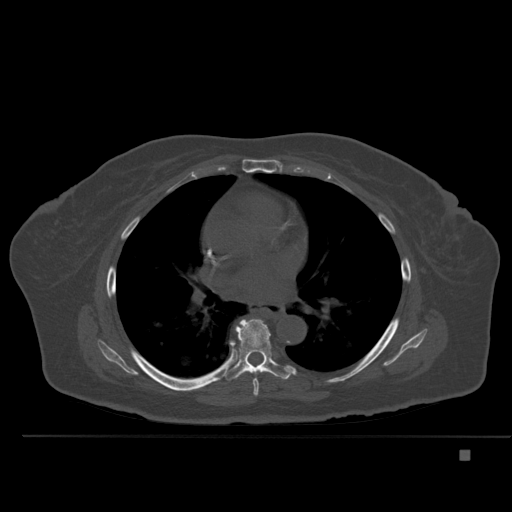
CT including the spine, one axial slice; slice 329 of 477 in the series (ordered by position); bone window (W 1800 / L 400 HU); 1.5 mm slice thickness; 512 × 512 image matrix, field of view 422 × 422 mm. Patient: female, 74 years. Case-level facts recorded for this patient, not image findings: primary cancer: colon.
Structures marked on this image (semi-automatically segmented with operator editing):
- T6 vertebra: bounding box <253,379,259,396> (left, top, right, bottom; pixels)
- T7 vertebra: <225,318,293,381>